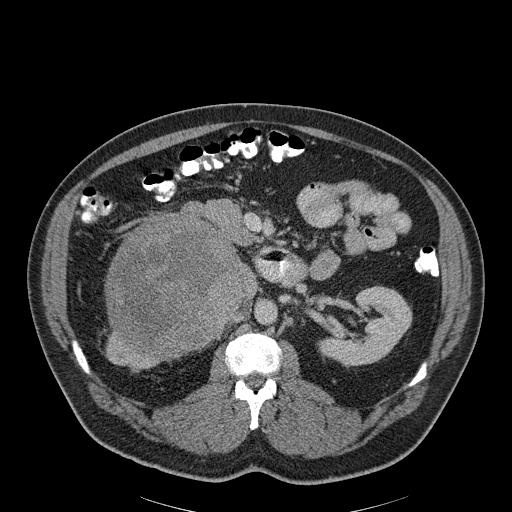
Contrast-enhanced abdominal CT, one axial slice; position 116 of 186 along the scan axis; reconstruction kernel B30f; 120 kVp; soft-tissue window (W 400 / L 40 HU); 3 mm slice thickness; 512 × 512 image matrix. Male patient, age 56 years. From the clinical record (not read from this slice): diagnosis: adrenocortical carcinoma; tumour side: right adrenal; tumour size at pathology: 18 cm; Ki-67 index: 2 %; stage (as recorded): 3.
Structures marked on this image (semi-automatic segmentation, software-assisted and operator-edited):
- mass: bounding box <107,216,242,356> (left, top, right, bottom; pixels)